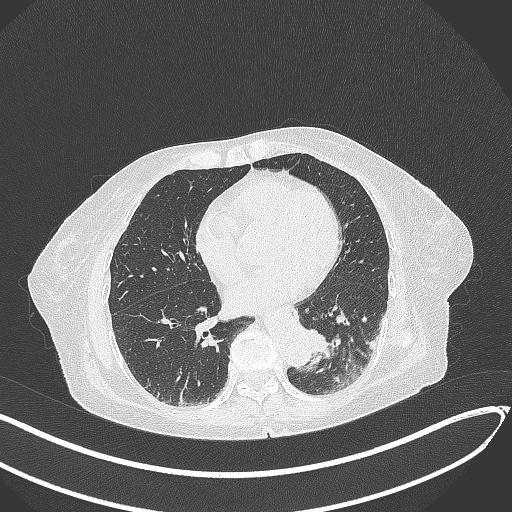
Chest CT, one axial slice; position 90 of 324 along the scan axis; lung window (W 1500 / L -600 HU); 1 mm slice thickness; 512 × 512 image matrix. Patient: female, 82 years. Case-level facts recorded for this patient, not image findings: clinical TNM (as recorded): T1b N0 M1.
Structures marked on this image (rectangle marked by the reading radiologist):
- lung tumour (recorded histology: adenocarcinoma): bounding box (x1, y1, x2, y2) in pixels: (300, 320, 335, 366)